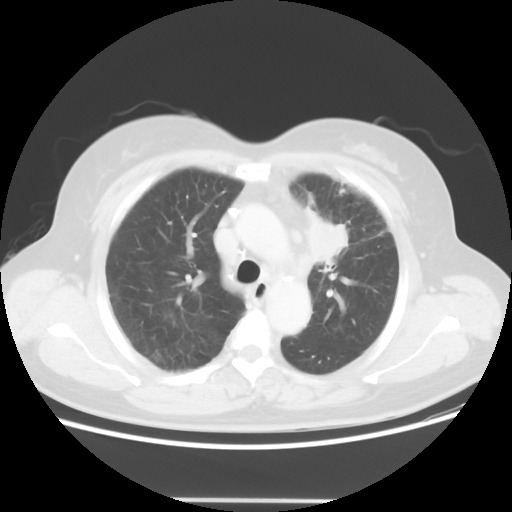
Chest CT, one axial slice. Position 39 of 52 along the scan axis. Reconstruction kernel STANDARD. 120 kVp. Lung window (W 1500 / L -600 HU). 512 × 512 image matrix, field of view 382 × 382 mm. Patient: female, 52 years. From the clinical record (not read from this slice): clinical TNM (as recorded): T2 N3 M0.
Outlined on this slice (rectangle marked by the reading radiologist):
- lung tumour (recorded histology: adenocarcinoma): box from (x=299, y=192) to (x=353, y=265) px